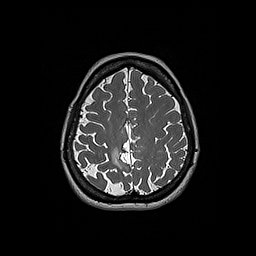
Brain MRI from a brain-tumour surgery series, one axial slice. Slice 56 of 192 in the series (ordered by position). 1 mm slice thickness. 256 × 256 image matrix, field of view 250 × 250 mm. From the clinical record (not read from this slice): histopathology: Oligodendroglioma; WHO grade: 2; IDH mutation: yes; tumour location: Right Parietal.
Outlined on this slice (outlined manually by an expert reader):
- tumour: box from (x=111, y=147) to (x=122, y=169) px